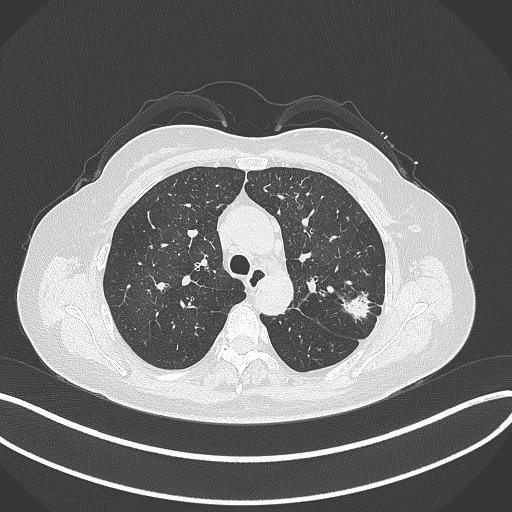
Chest CT, one axial slice; reconstruction kernel B70f; 120 kVp; lung window (W 1500 / L -600 HU); 1 mm slice thickness; 512 × 512 image matrix, field of view 400 × 400 mm. Female patient, age 60 years. From the clinical record (not read from this slice): clinical TNM (as recorded): T1c N0 M0.
Outlined on this slice (bounding box drawn by a radiologist):
- lung tumour (recorded histology: adenocarcinoma): box from (x=338, y=288) to (x=373, y=321) px